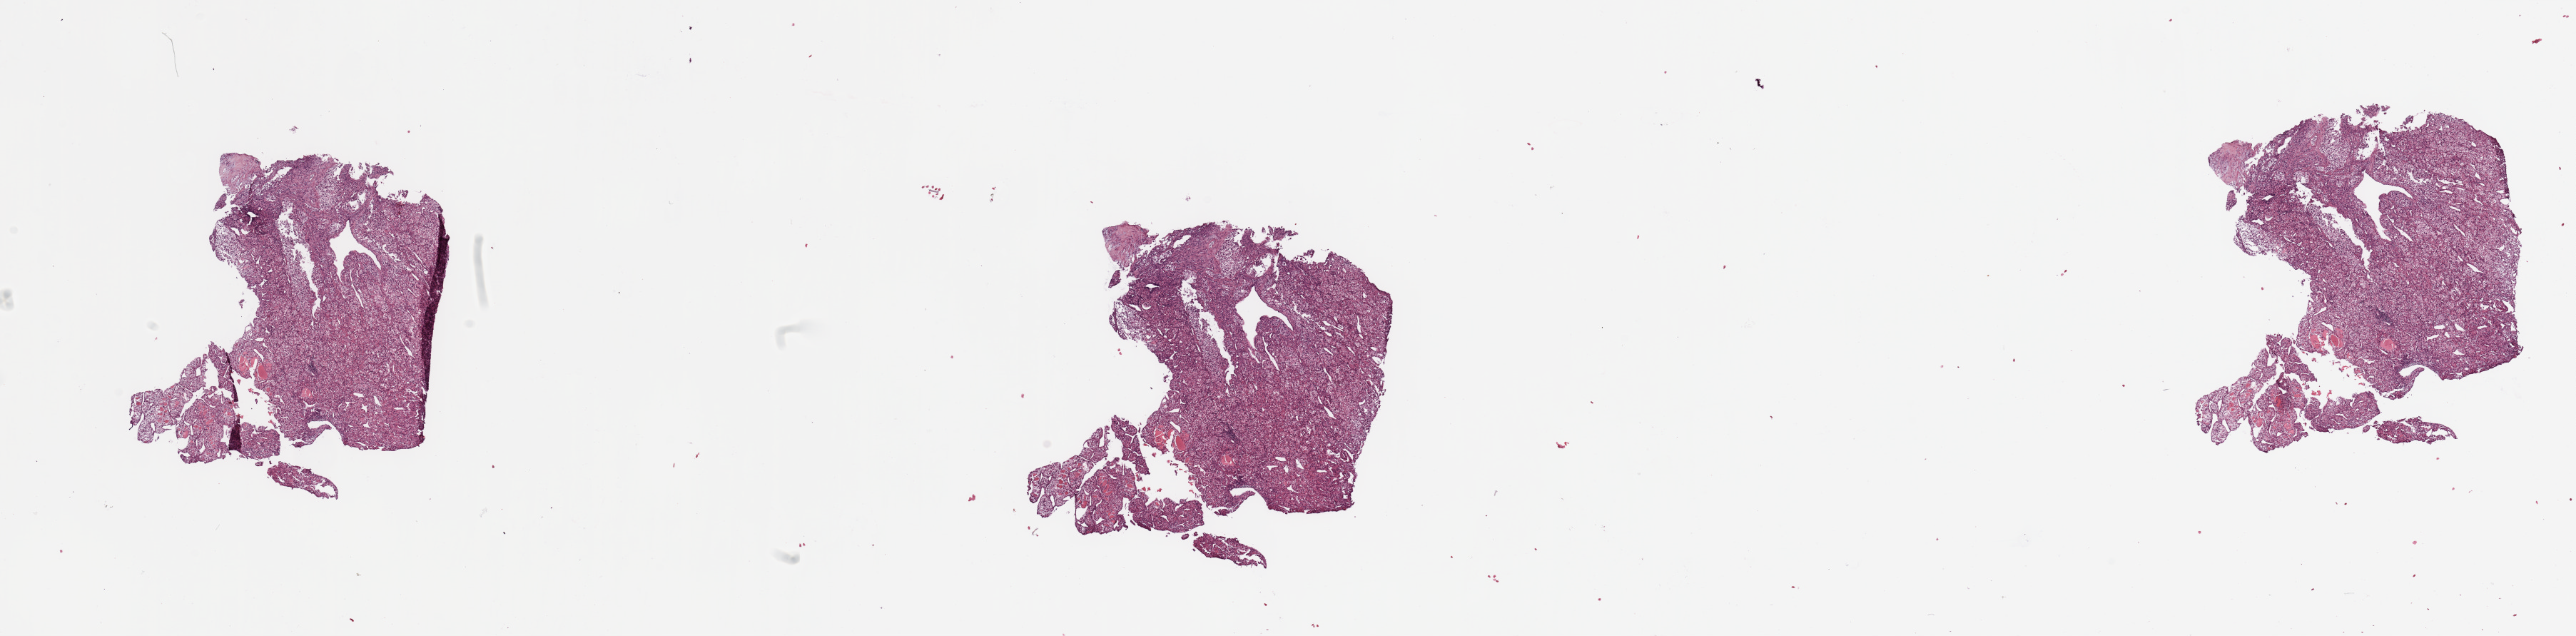
H&E whole-slide image — low-resolution overview of the scanned area, about 28.5 x 7.0 mm; kidney, tumour tissue. Patient: male, age 58 years. Histologic grade: G3 (poorly differentiated).
Diagnosis: Renal cell carcinoma, NOS. AJCC pathologic stage: II.